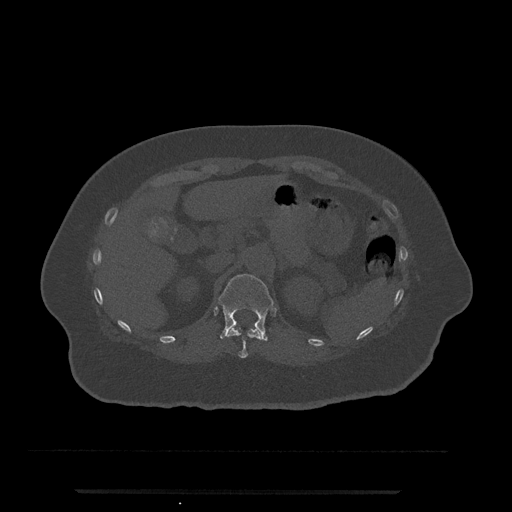
CT including the spine, one axial slice. Slice 191 of 797 in the series (ordered by position). Reconstruction kernel Br40s/3. 120 kVp. Bone window (W 1800 / L 400 HU). 0.5 mm slice thickness. 512 × 512 image matrix. Female patient, age 51 years. From the clinical record (not read from this slice): primary cancer: neuro; vertebrae with lytic lesions (as recorded): T8.
Annotated regions visible in this slice (semi-automatically segmented with operator editing):
- T11 vertebra: box from (x=226, y=327) to (x=261, y=358) px
- T12 vertebra: (x=218, y=274)–(x=274, y=341)